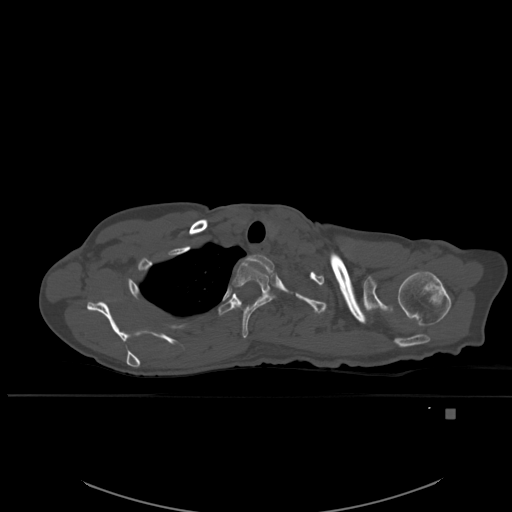
CT including the spine, one axial slice. Position 433 of 537 along the scan axis. Bone window (W 1800 / L 400 HU). 1.5 mm slice thickness. 512 × 512 image matrix, field of view 440 × 440 mm. Patient: female, 45 years. From the clinical record (not read from this slice): primary cancer: lung.
Outlined on this slice (semi-automatically segmented with operator editing):
- T1 vertebra: bounding box (x1, y1, x2, y2) in pixels: (240, 255, 276, 274)
- T2 vertebra: (230, 259, 274, 338)
- T3 vertebra: (218, 292, 260, 315)